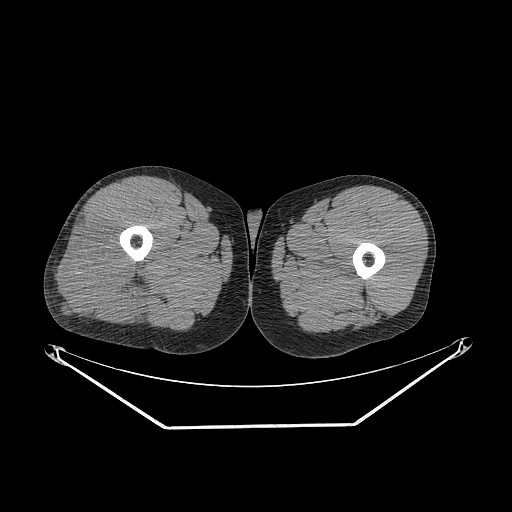
CT of an extremity soft-tissue mass (from a PET/CT study), one axial slice; slice 253 of 267 in the series (ordered by position); 140 kVp; soft-tissue window (W 400 / L 40 HU); 512 × 512 image matrix, field of view 500 × 500 mm. Male patient. Case-level facts recorded for this patient, not image findings: histological type: poorly differentiated synovial sarcoma; grade: high; site of the primary tumour: right buttock.
Annotated regions visible in this slice (expert contour drawn on MRI and transferred to this co-registered scan by the dataset authors):
- gross tumour volume including surrounding oedema: bounding box <59,219,152,321> (left, top, right, bottom; pixels)
- gross tumour volume (mass): <59,219,152,321>